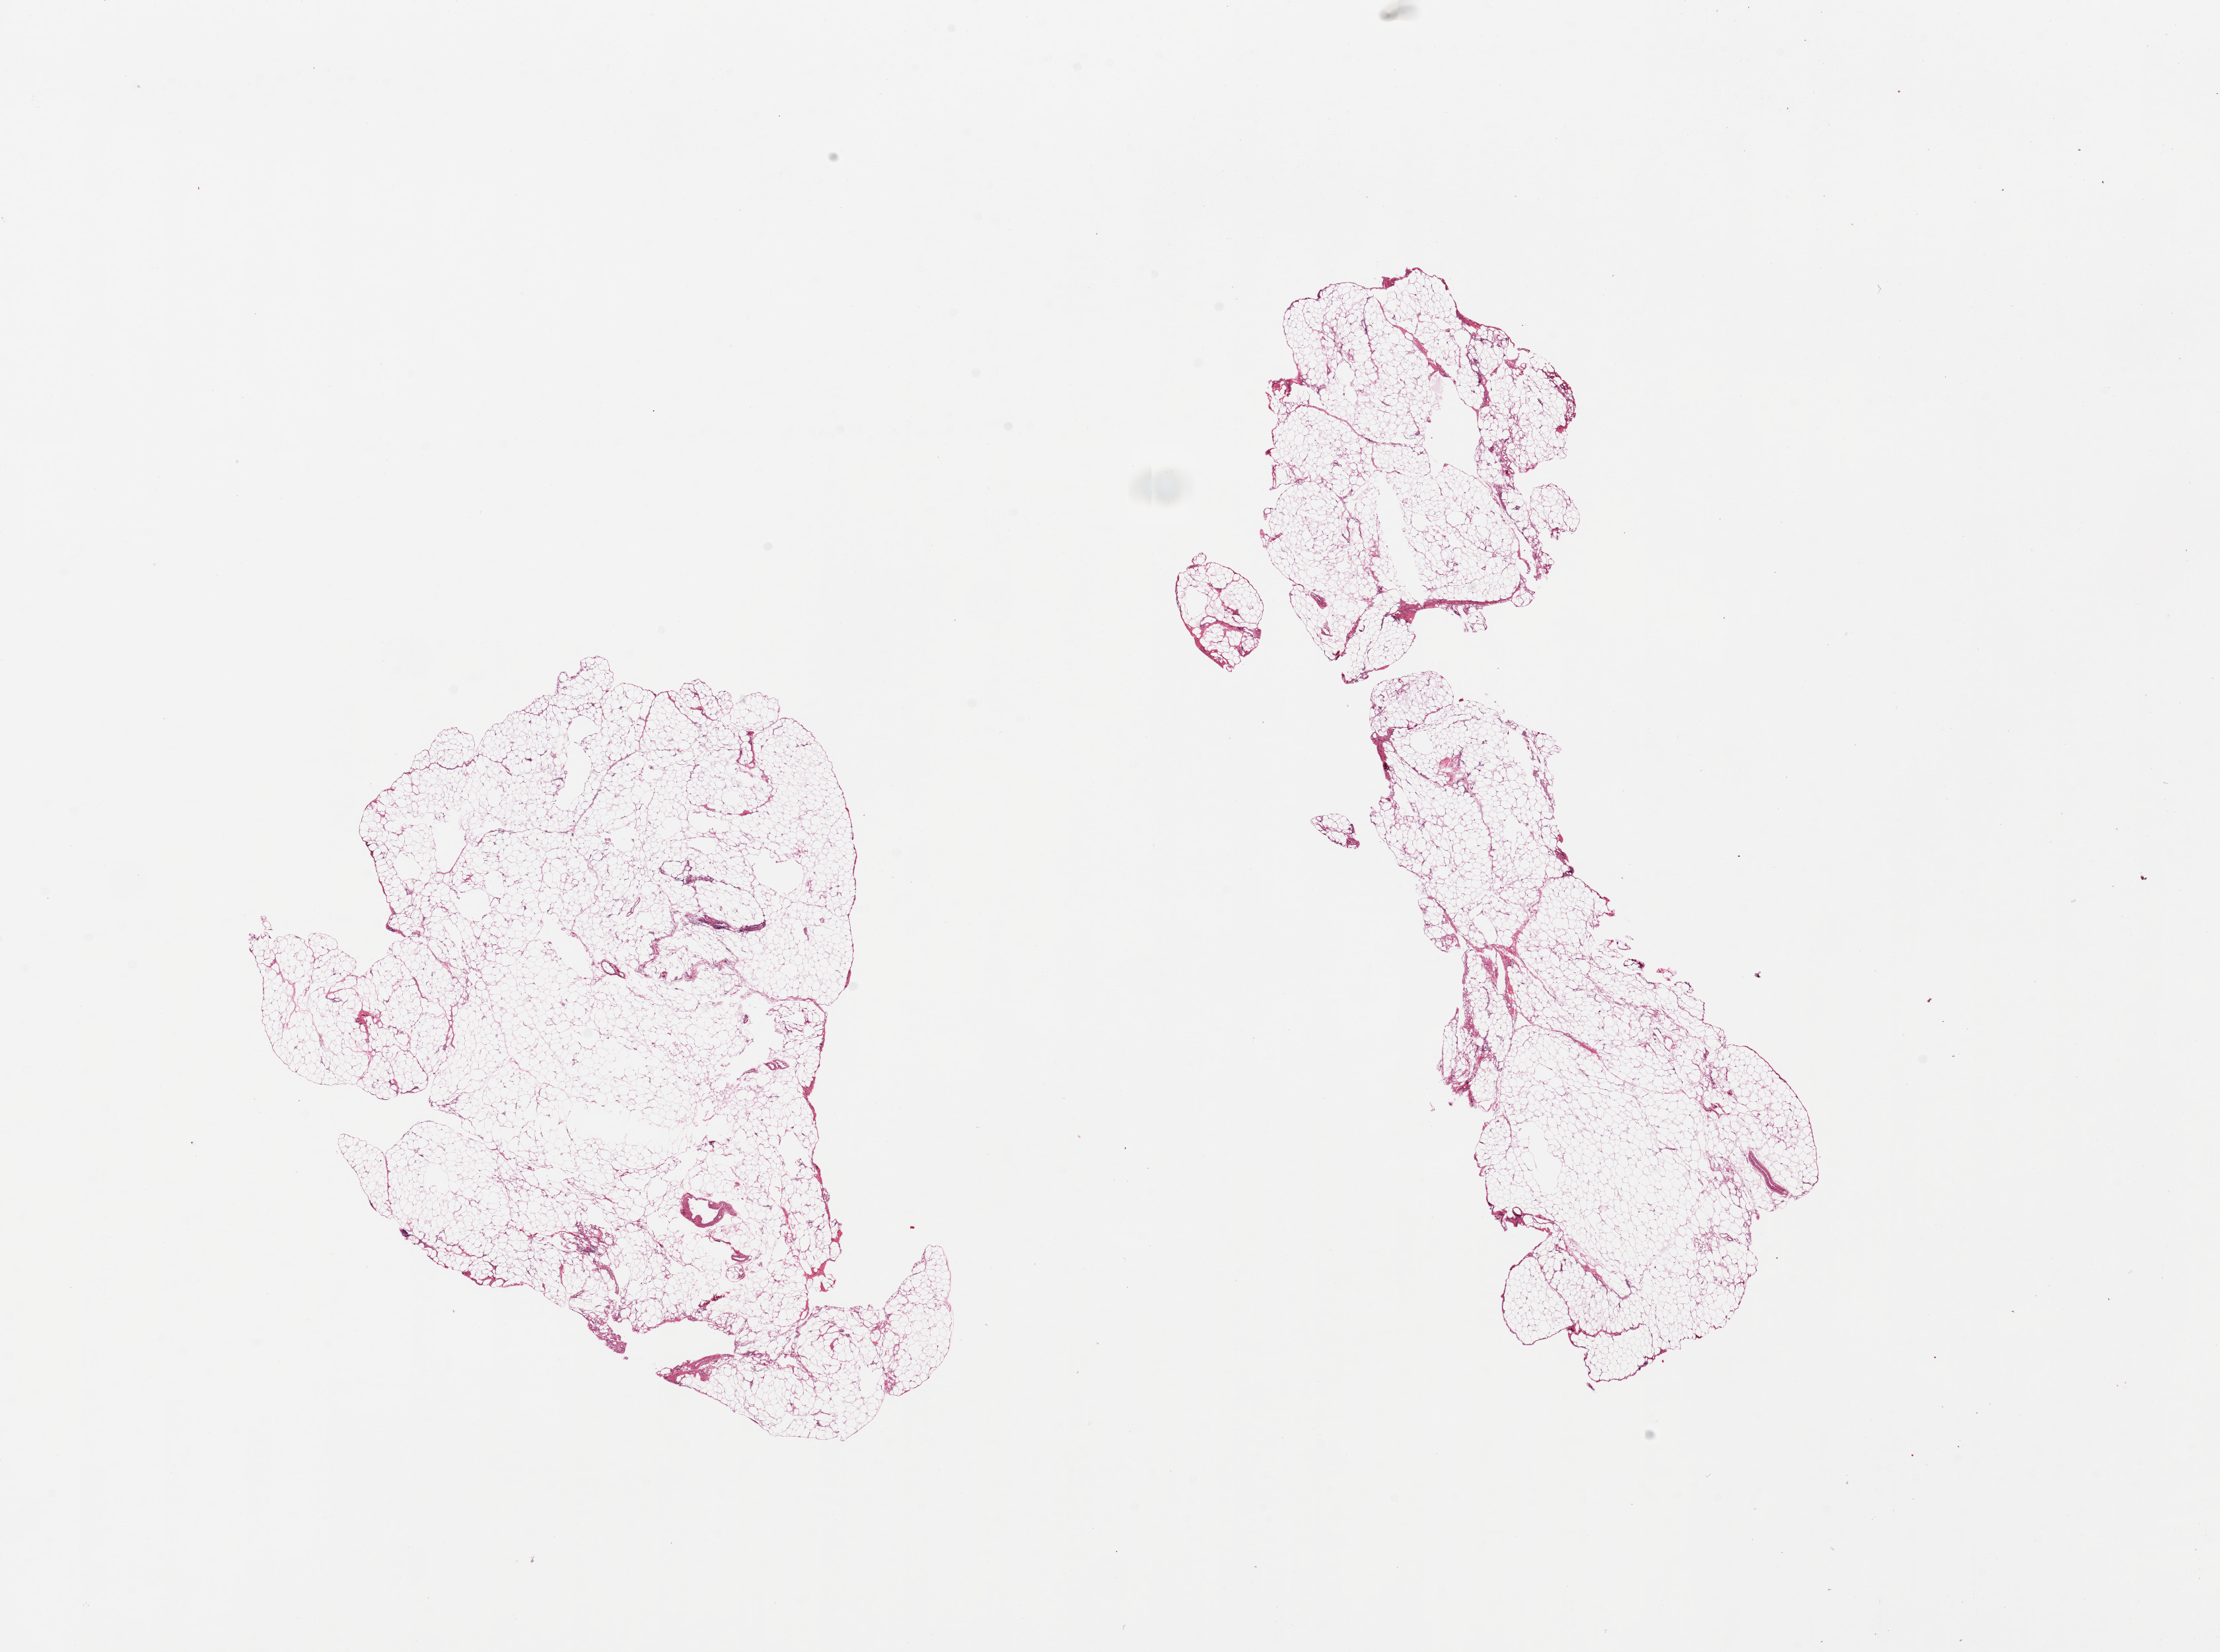
H&E whole-slide image — shown as a low-resolution overview of the whole scanned area (about 26.6 x 19.8 mm, from a 20x scan), PAXgene-fixed, paraffin-embedded tissue, section of omentum (target tissue), tissue donor sample. Donor: male.
Pathologist's review note for this sample: 2 pieces.